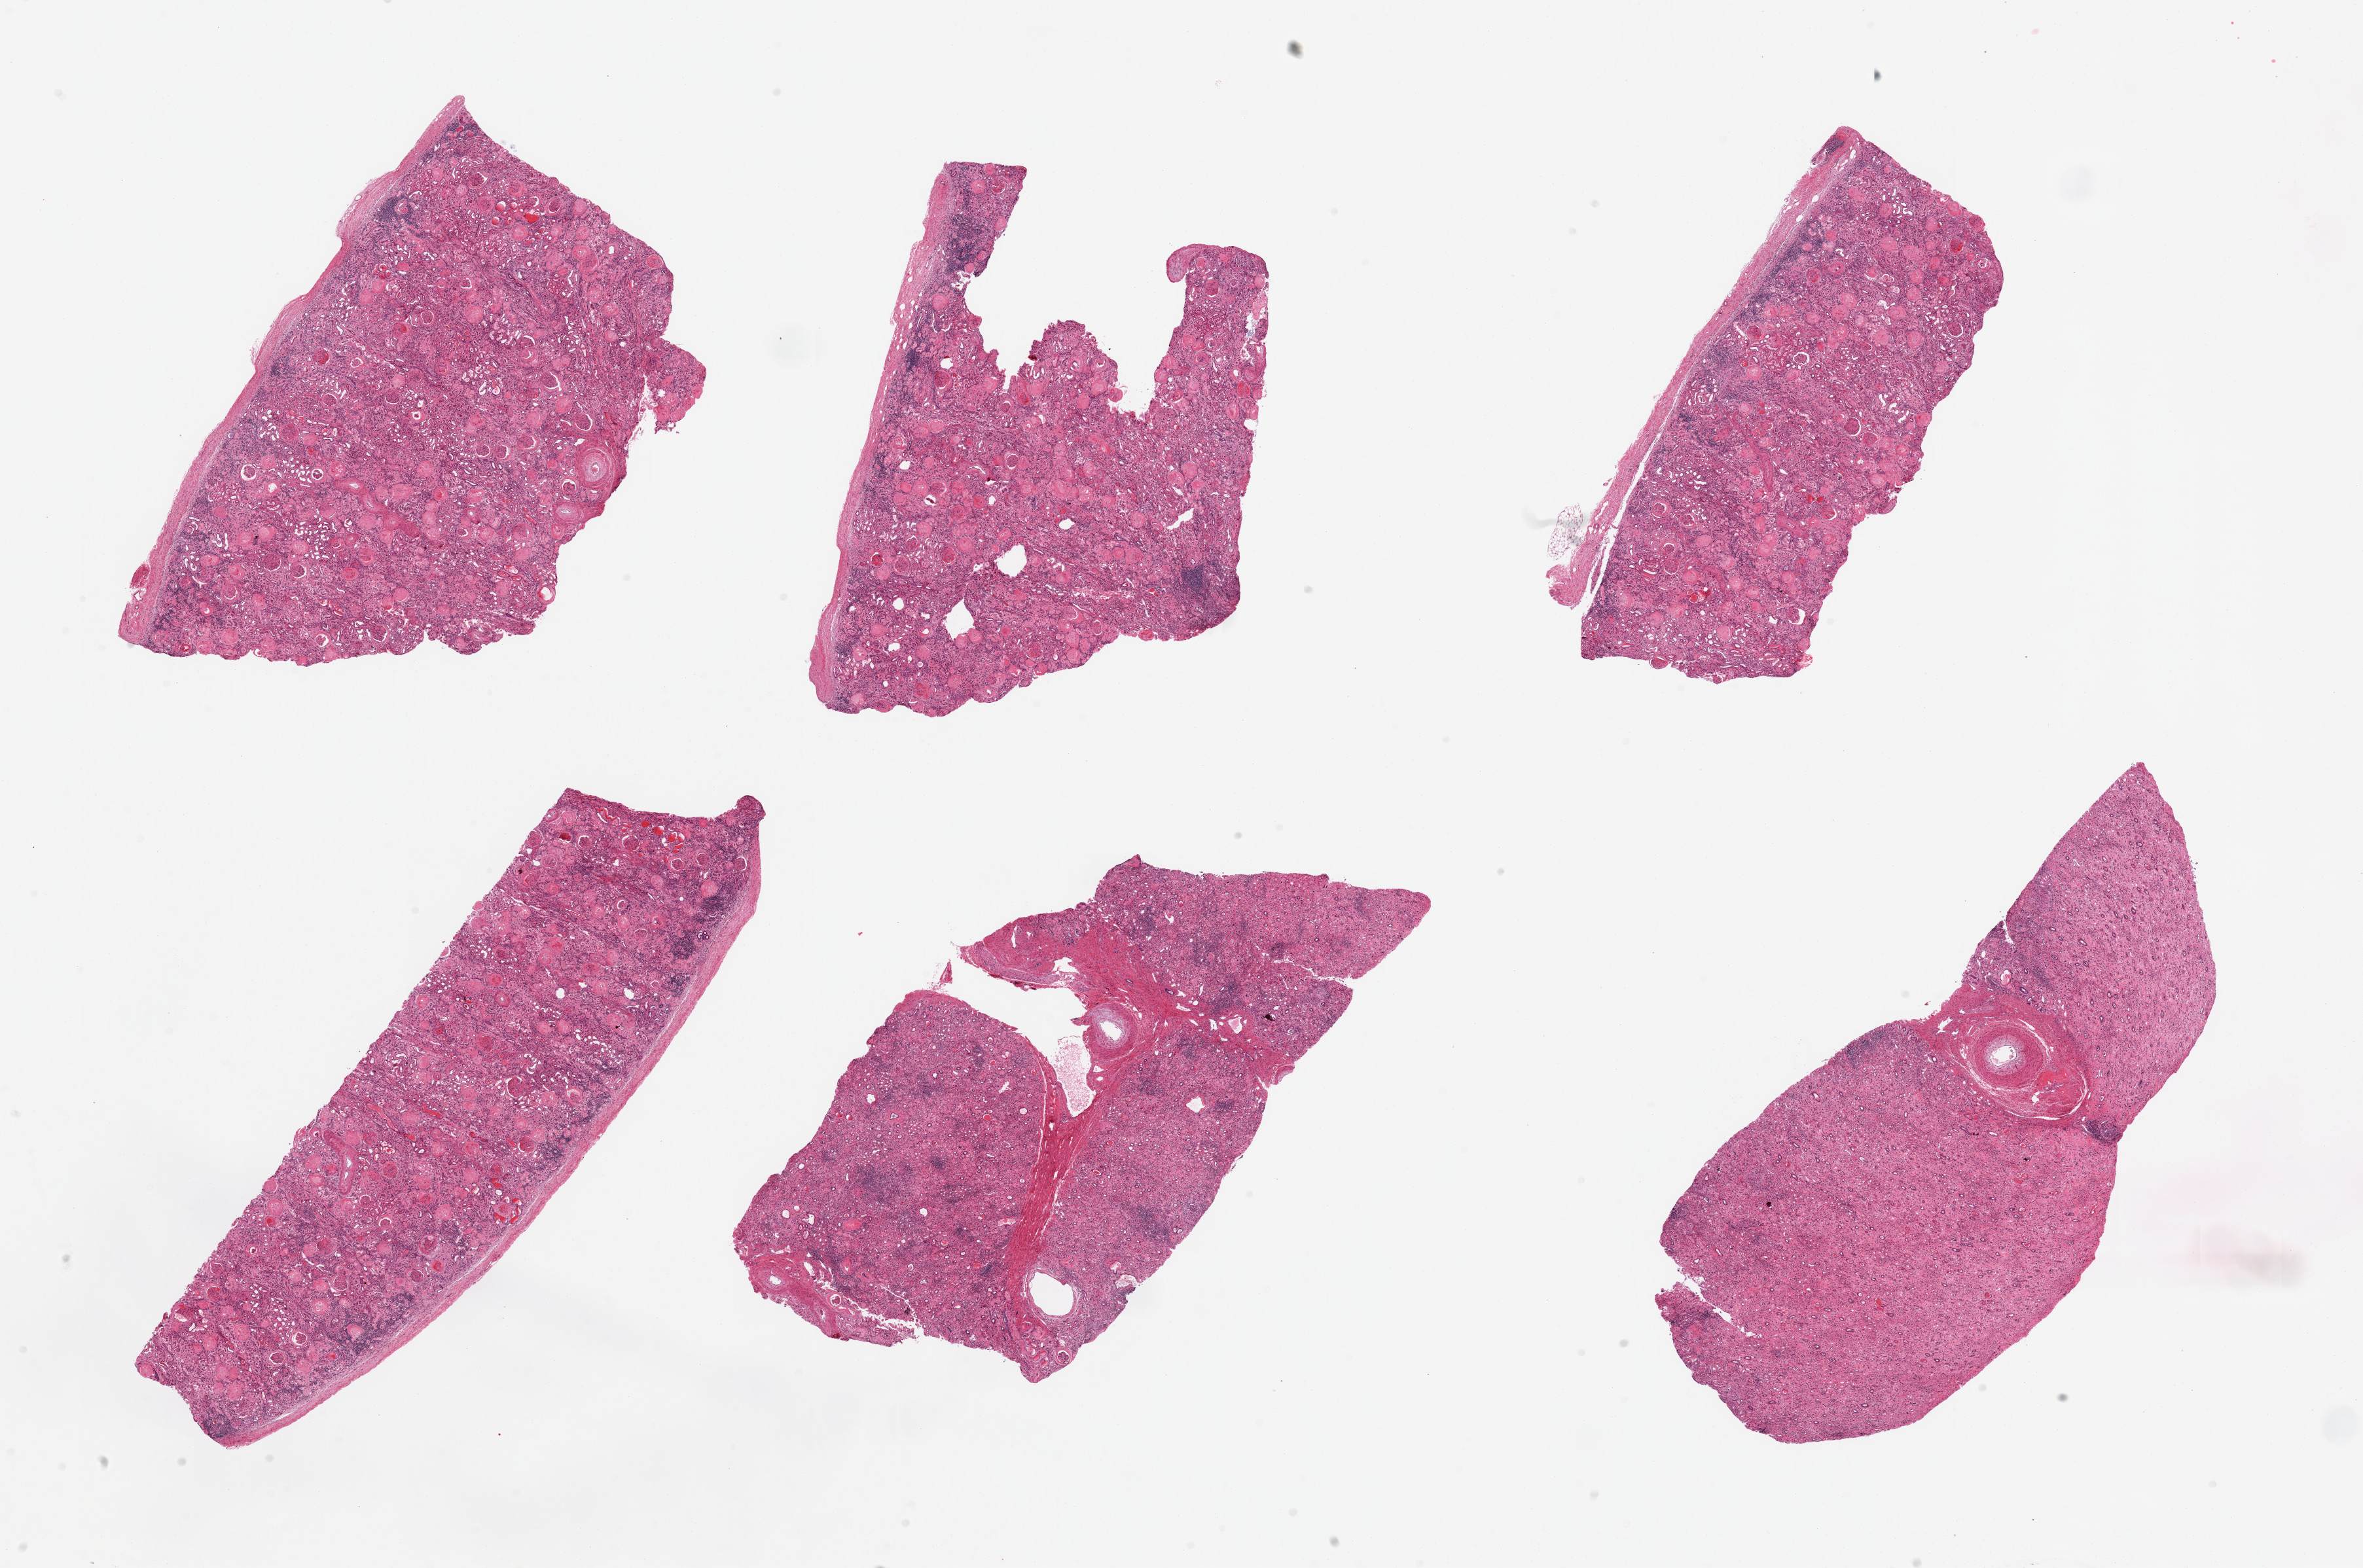
Digitized hematoxylin and eosin (H&E)-stained section, whole scanned area (about 28.5 x 18.9 mm, acquisition: 20x scan) shown as a low-resolution overview. PAXgene-fixed paraffin-embedded (PFPE) section. Section of renal cortex (target tissue). Donor tissue sample.
Pathologist's review note for this sample: 6 pieces; diabetic nephropathy, arterio and arteriolo-nephrosclerosis; interstitial nephritis; end stage renal disease.